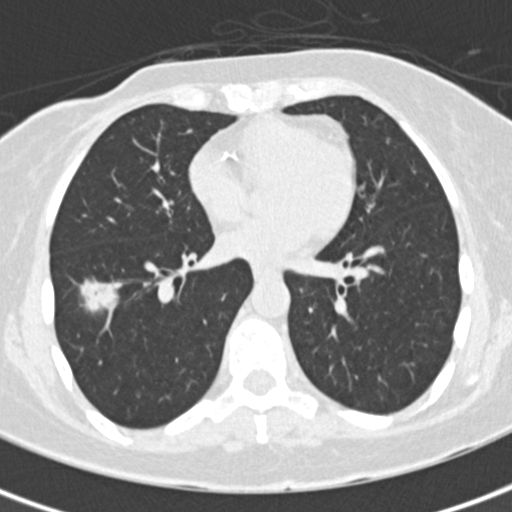
Chest CT (low-dose screening protocol), one axial image. Baseline screening round. Lung window (W 1500 / L -600 HU). 2 mm slice thickness. Standard (soft-tissue) reconstruction kernel (B30f). 120 kVp. Slice 95 of 171 in the series. 512 × 512 image matrix. Female, age 56 years at enrolment.
Expert reader's lesion annotation, bounding box [x1, y1, x2, y2] px = [70, 273, 130, 328]. The screening reader recorded 5 non-calcified nodules or masses ≥4 mm on this exam (right lower lobe, right upper lobe, left upper lobe, left lower lobe, left lower lobe); which of them this box marks is not recorded. Official screen result: positive, change unspecified: nodule(s) >= 4 mm or enlarging nodule(s), mass(es), or other non-specific abnormalities suspicious for lung cancer. Later outcome: lung cancer diagnosed 26 days after this screen — bronchiolo-alveolar carcinoma, mucinous, right lower lobe, well differentiated (G1), stage IA (AJCC 6th edition), 19 mm at pathology.